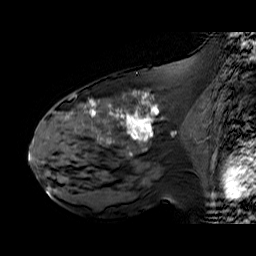
Breast MRI (dynamic contrast-enhanced), one sagittal slice; slice 31 of 60 in the series (ordered by position); dynamic contrast-enhanced series, time point 2 of 6 at this slice position (early post-contrast); 1.5 T; TE 6.3 ms, TR 32.9 ms; 4 mm slice thickness; 256 × 256 image matrix. Female patient. Case-level facts recorded for this patient, not image findings: setting: breast cancer imaged before/during neoadjuvant chemotherapy; receptor status: HER2-positive.
Outlined on this slice (semi-automatic segmentation, software-assisted and operator-edited):
- analysis volume of interest (the breast-tissue region the enhancement analysis was run in; not a lesion): bounding box <48,92,195,174> (left, top, right, bottom; pixels)
- tumour enhancement mask (voxels above the 100 % enhancement threshold inside the analysis volume of interest): <66,92,152,143>